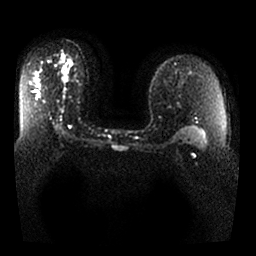
Breast MRI, one axial slice; slice 16 of 25 in the series (ordered by position); diffusion-weighted series; image 2 of 4 stored at this slice position (different b-values; order by instance number); 1.5 T; 4 mm slice thickness; 256 × 256 image matrix, field of view 340 × 340 mm. Female patient.
Outlined on this slice (expert manual segmentation):
- tumour on diffusion-weighted imaging: bounding box [x1, y1, x2, y2] px = [63, 68, 68, 82]